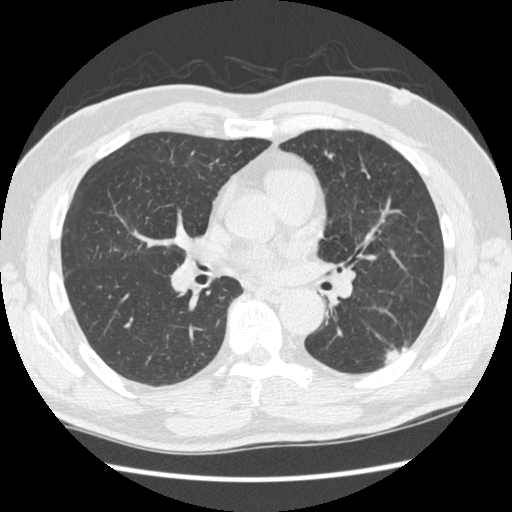
Axial slice from a low-dose chest CT screening exam; first (baseline) screen; lung window (W 1500 / L -600 HU); 1.25 mm slice thickness; 120 kVp; 512 × 512 image matrix. Male participant, aged 74 years at enrolment. Former smoker at enrolment.
Expert-annotated lung lesion, bounding box <373,324,415,370> (left, top, right, bottom; pixels). The screening reader recorded 3 non-calcified nodules or masses ≥4 mm on this exam (right upper lobe, right lower lobe, left upper lobe); which of them this box marks is not recorded. Later outcome: lung cancer diagnosed 384 days after this screen — squamous cell carcinoma, NOS, left lower lobe, well differentiated (G1), stage IA (AJCC 6th edition), 28 mm at pathology.